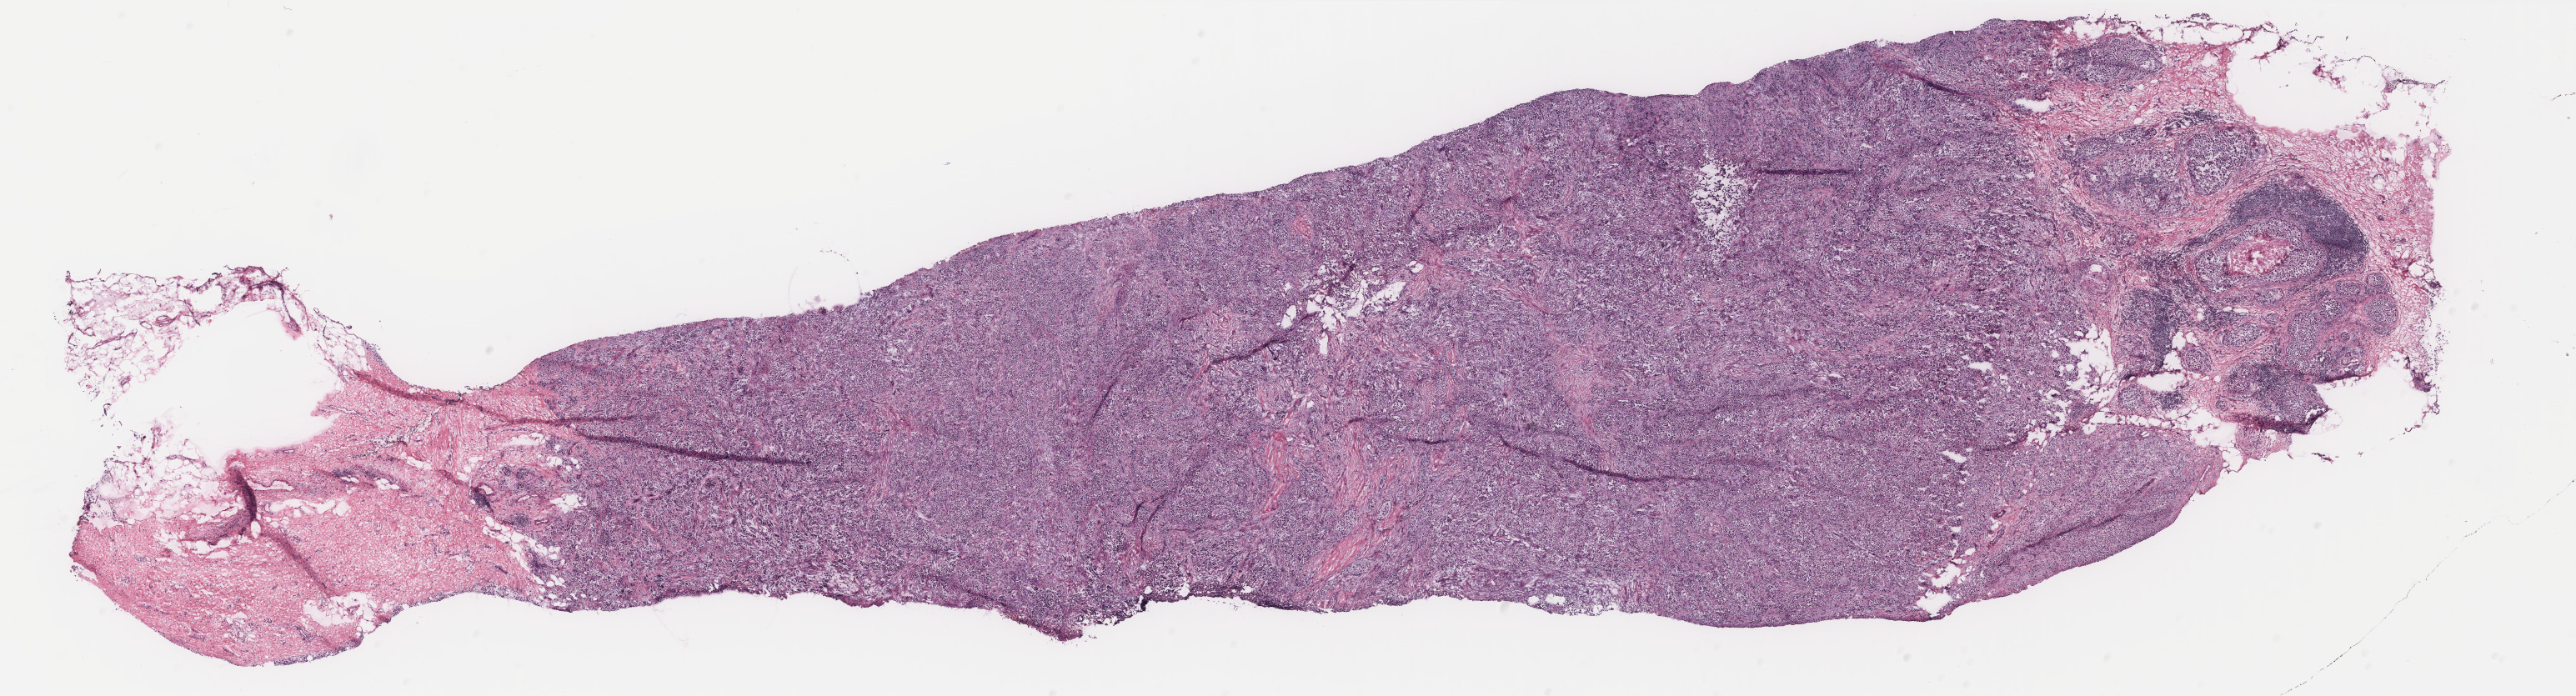
Whole-slide histology image, H&E-stained, shown as a low-resolution overview of the whole scanned area (about 24.7 x 6.7 mm); tumour tissue sample, breast. Patient: female, age 75 years.
* AJCC pathologic stage: IIA
* histologic diagnosis: Infiltrating duct carcinoma, NOS